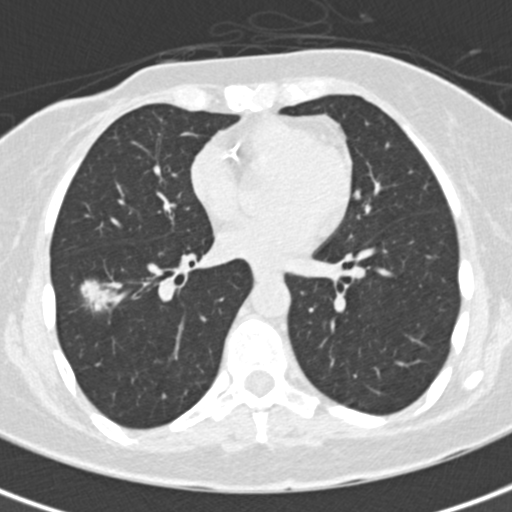
Low-dose screening chest CT, one axial slice. Slice 78 of 171 in the series (ordered by position). Lung window (W 1500 / L -600 HU). 512 × 512 image matrix, field of view 284 × 284 mm.
Annotated regions visible in this slice (manually delineated by an expert):
- lesion 1 (tumor, lower lobe of right lung): box from (x=80, y=279) to (x=122, y=311) px